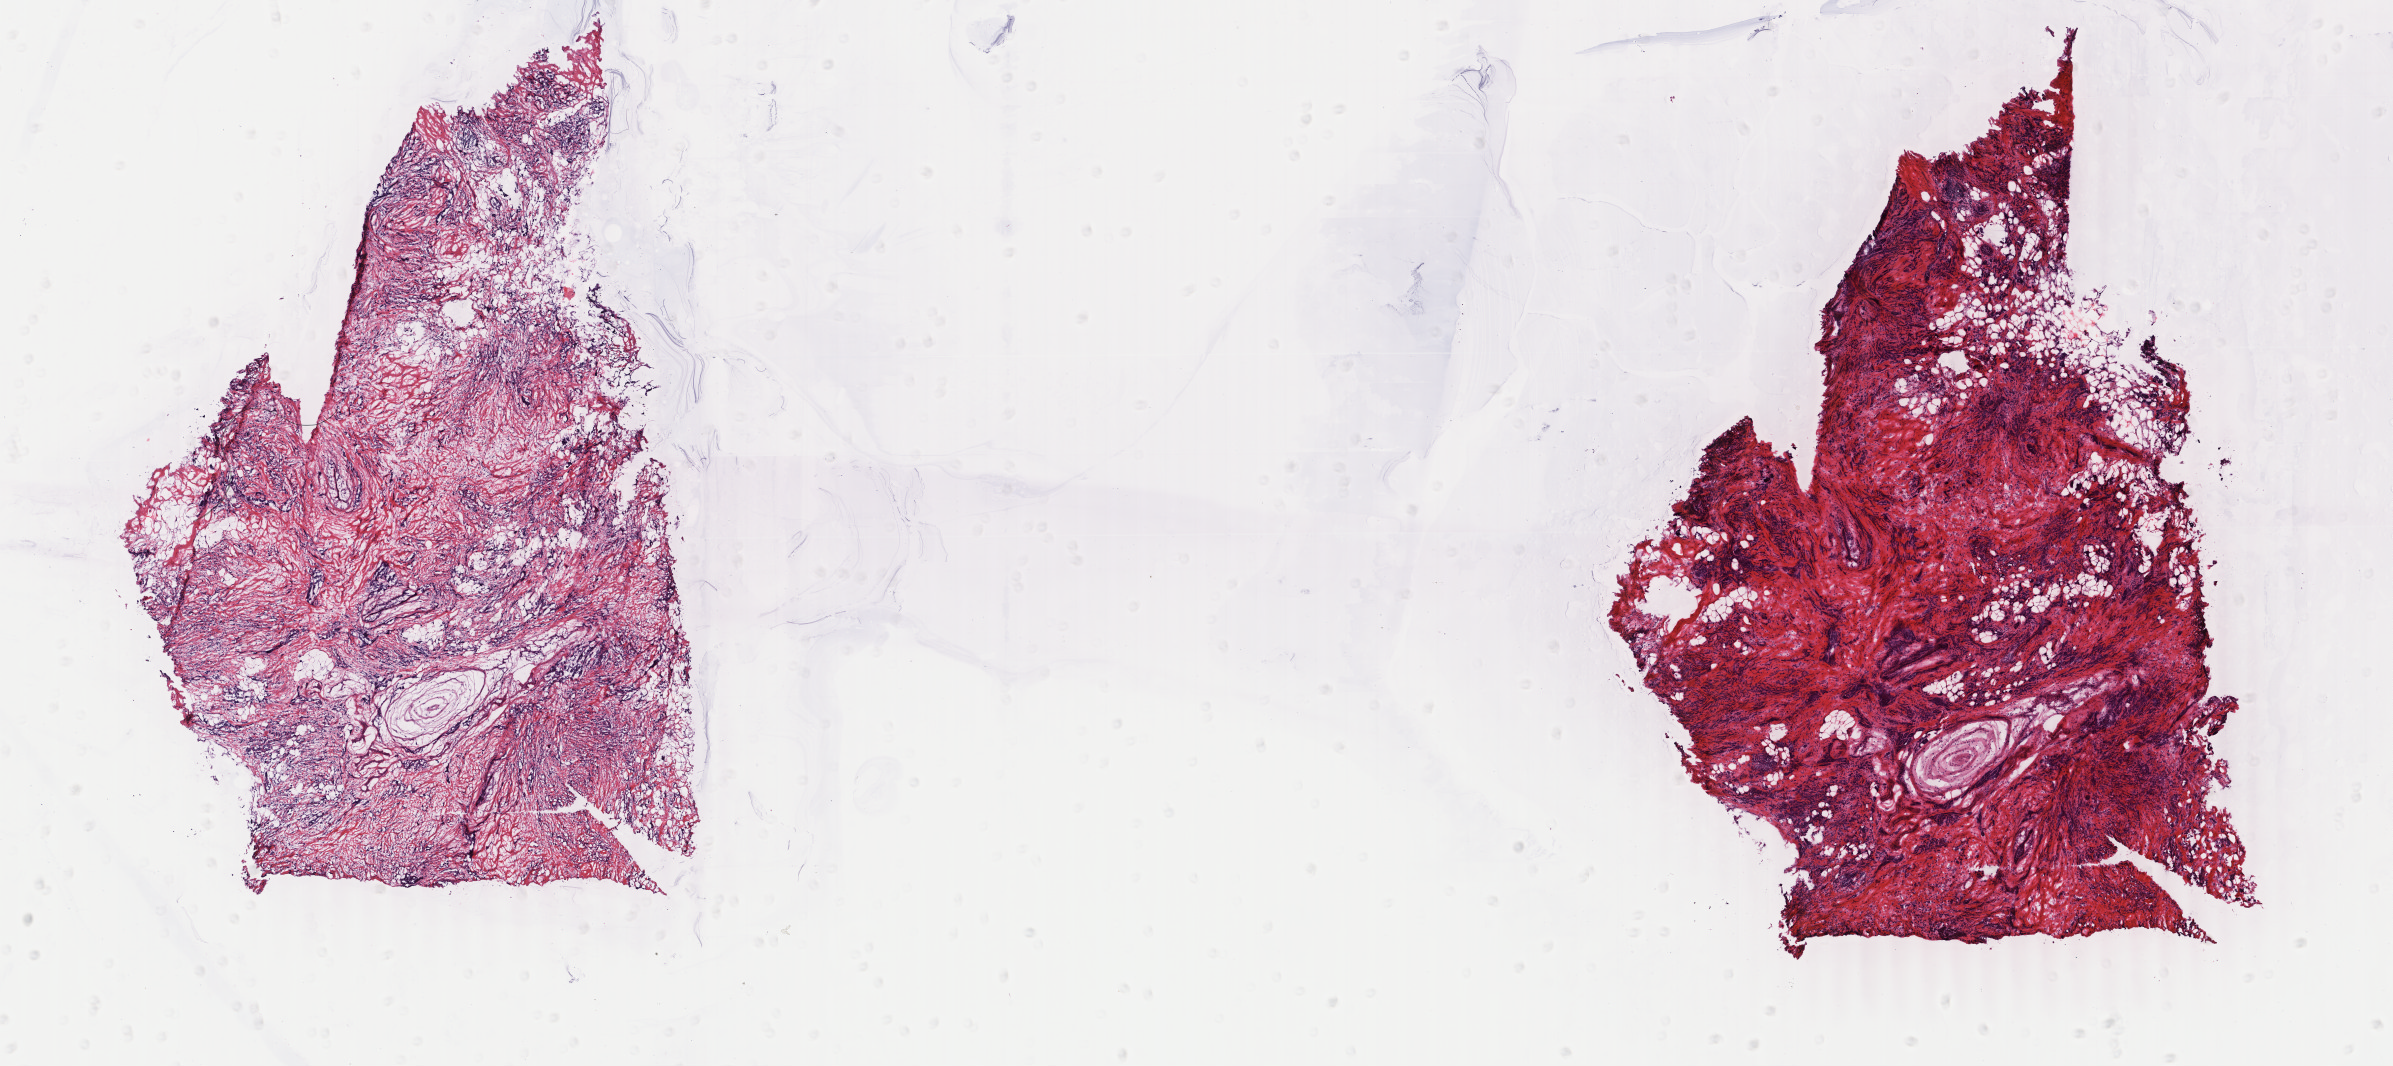
Digitized H&E-stained tissue section (whole slide) — shown as a low-resolution overview of the whole scanned area (about 19.0 x 8.5 mm). Frozen section from the bottom of the tissue portion. Breast, primary tumour sample. Female, age 60 years at initial diagnosis. Pathologist review of this section (percent, as recorded): tumour cells 40%, tumour nuclei 80%, normal cells 3%, stromal cells 57%, necrosis 0%. Infiltration values recorded for this section: lymphocyte infiltration 0%, monocyte infiltration 0%, neutrophil infiltration 0%.
Pathologic diagnosis: Lobular carcinoma, NOS. Laterality: right. AJCC pathologic stage: IIIA (5th edition). Lymph nodes positive (case pathology): 4 of 20 examined.